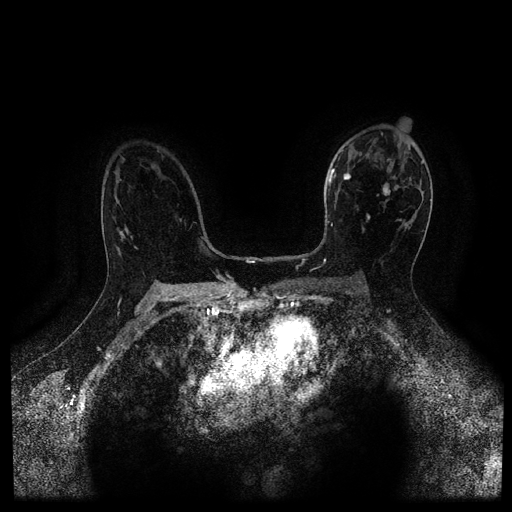
Breast MRI (dynamic contrast-enhanced, multi-phase), one axial slice. Slice 66 of 116 in the series (ordered by position). Dynamic contrast-enhanced series, time point 2 of 5 at this slice position (early post-contrast). 1.5 T. TE 2.7 ms, TR 5.4 ms. 2 mm slice thickness. 512 × 512 image matrix. Female patient, age 50 years.
Outlined on this slice (semi-automatic segmentation, software-assisted and operator-edited):
- breast lesion (labelled 'tumour' in the annotation; benign lesions carry a separate 'benign' label): bounding box <340,172,400,222> (left, top, right, bottom; pixels)